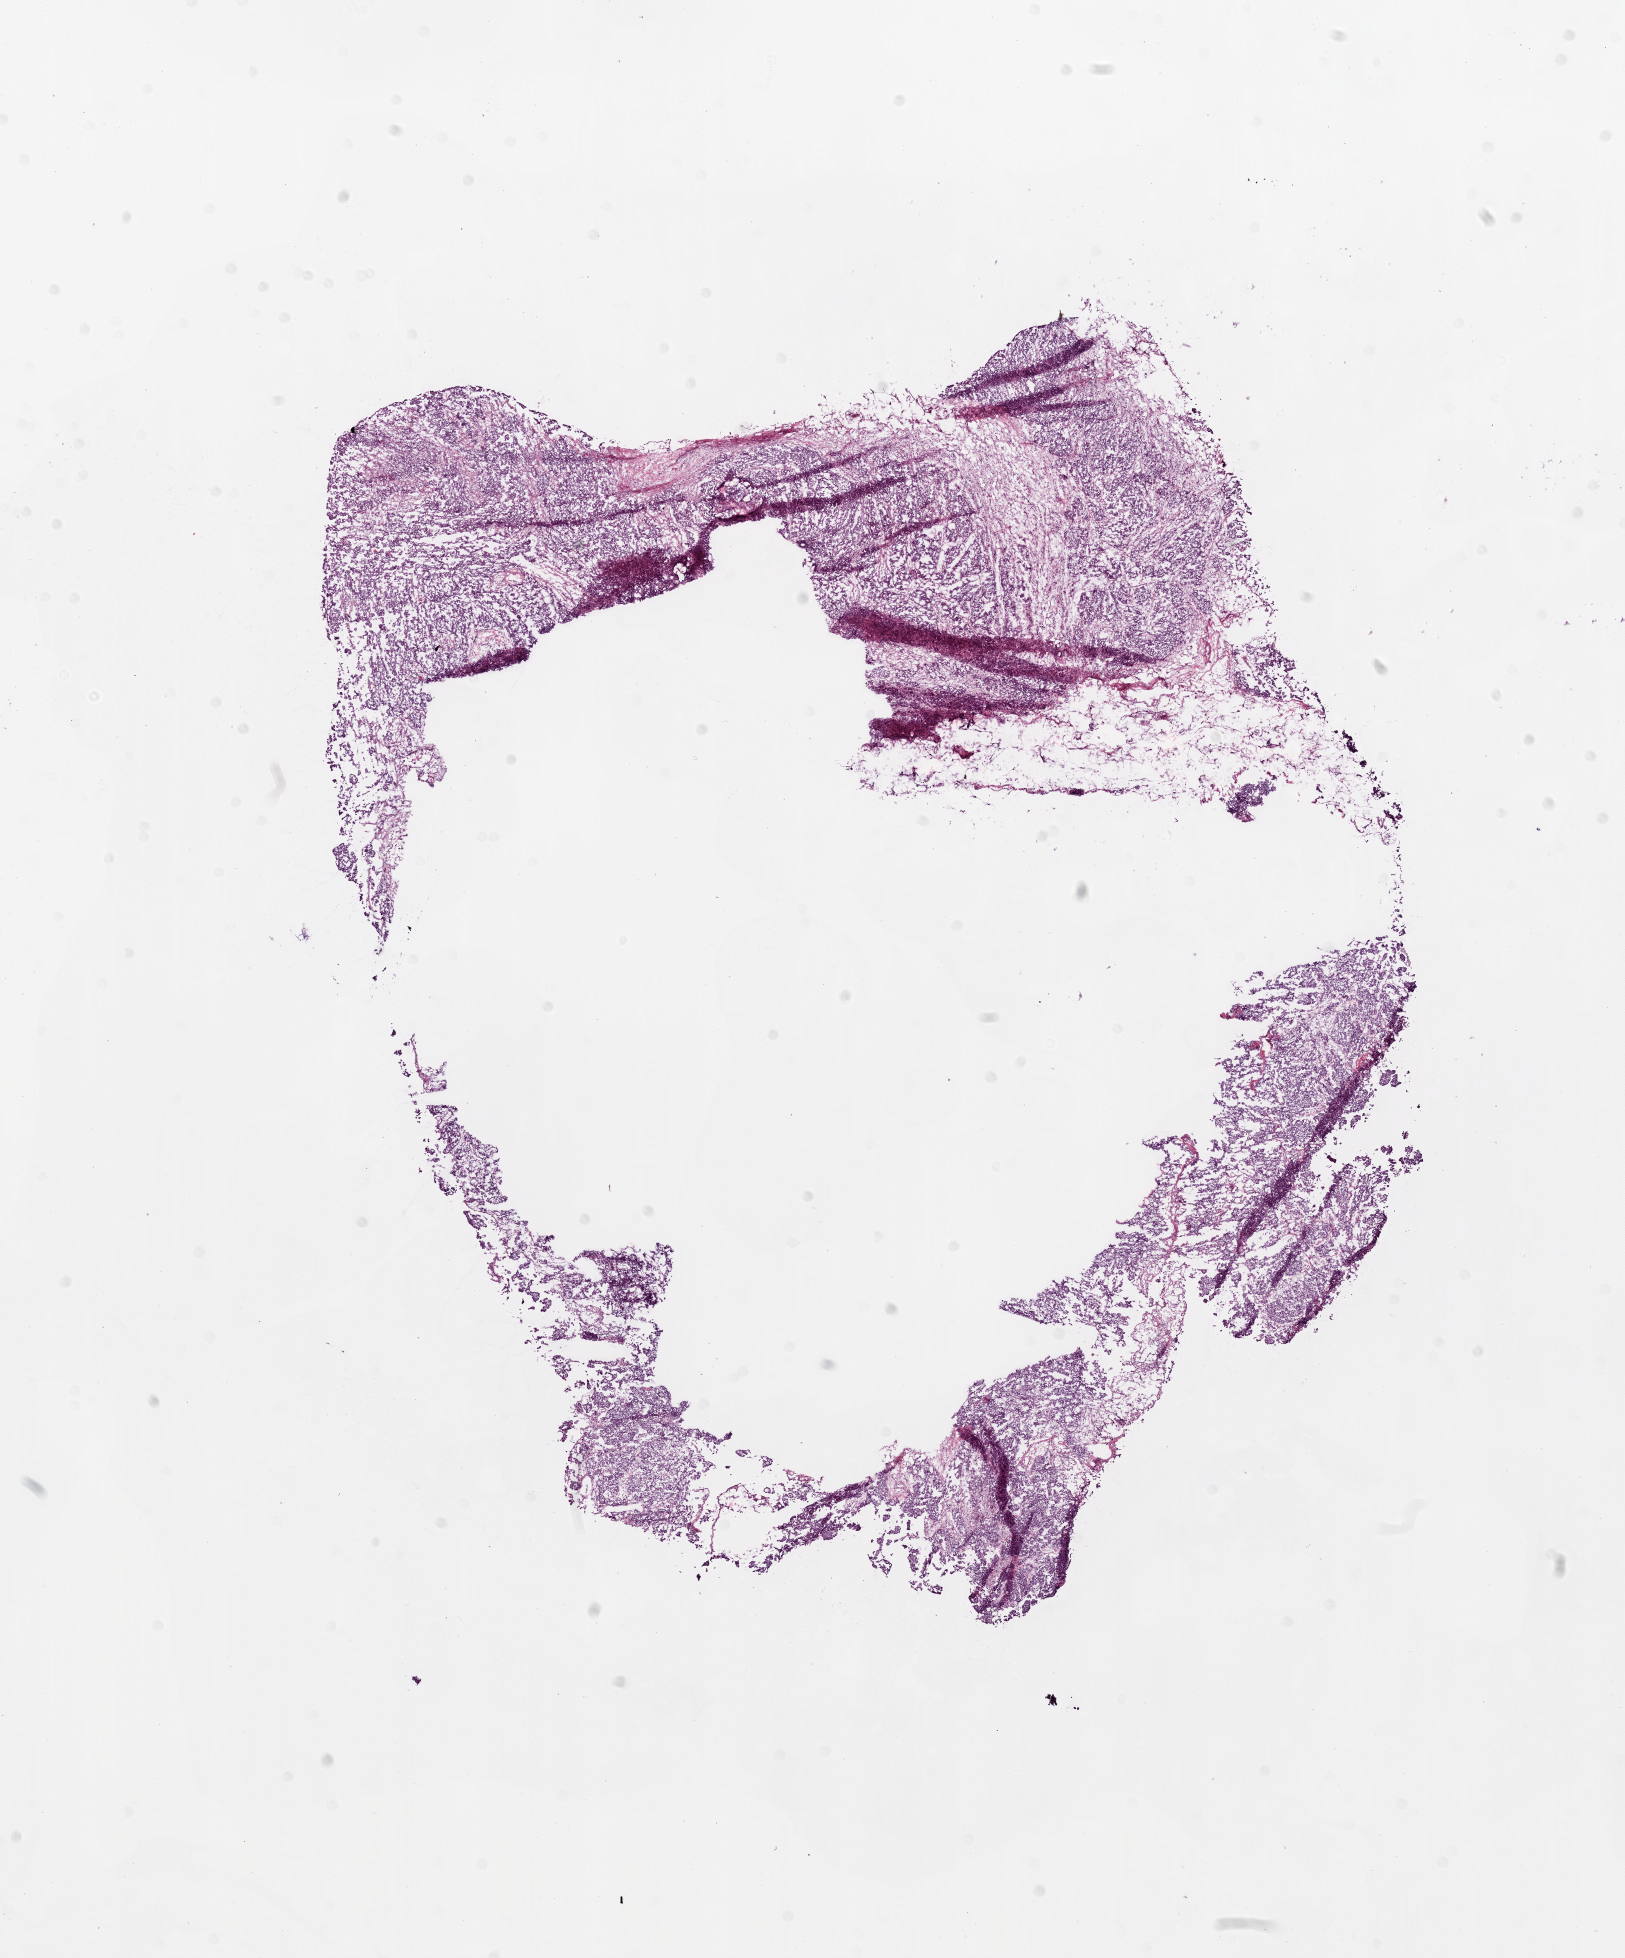
Digitized H&E-stained tissue section (whole slide), whole scanned area (about 13.0 x 15.7 mm, slide scanned at 20x) shown as a low-resolution overview. Frozen section from the bottom of the tissue portion. Ovary, primary tumour sample. Female, age 40 years at initial diagnosis. Histologic grade: G3 (poorly differentiated). Pathologist review of this section (percent, as recorded): tumour cells 85%, tumour nuclei 80%, normal cells 0%, stromal cells 15%, necrosis 0%. Infiltration values recorded for this section: lymphocyte infiltration 2%.
Diagnosis: Serous cystadenocarcinoma, NOS. FIGO stage: IIIC.